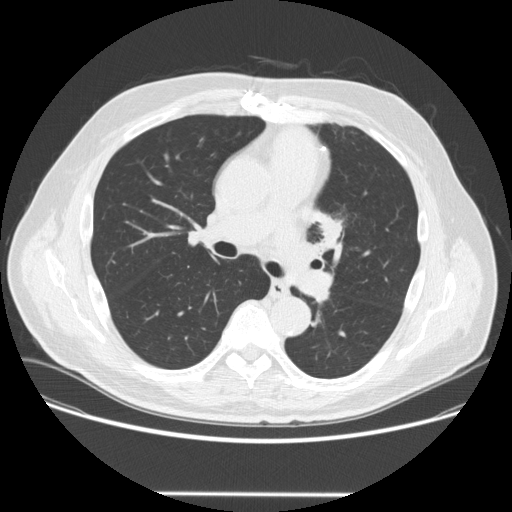
Low-dose screening chest CT, one axial slice. Slice 157 of 253 in the series (ordered by position). 120 kVp. Lung window (W 1500 / L -600 HU). 512 × 512 image matrix, field of view 400 × 400 mm.
Structures marked on this image (manually delineated by an expert):
- lesion 1 (tumor, upper lobe of left lung): bounding box (x1, y1, x2, y2) in pixels: (321, 218, 342, 245)